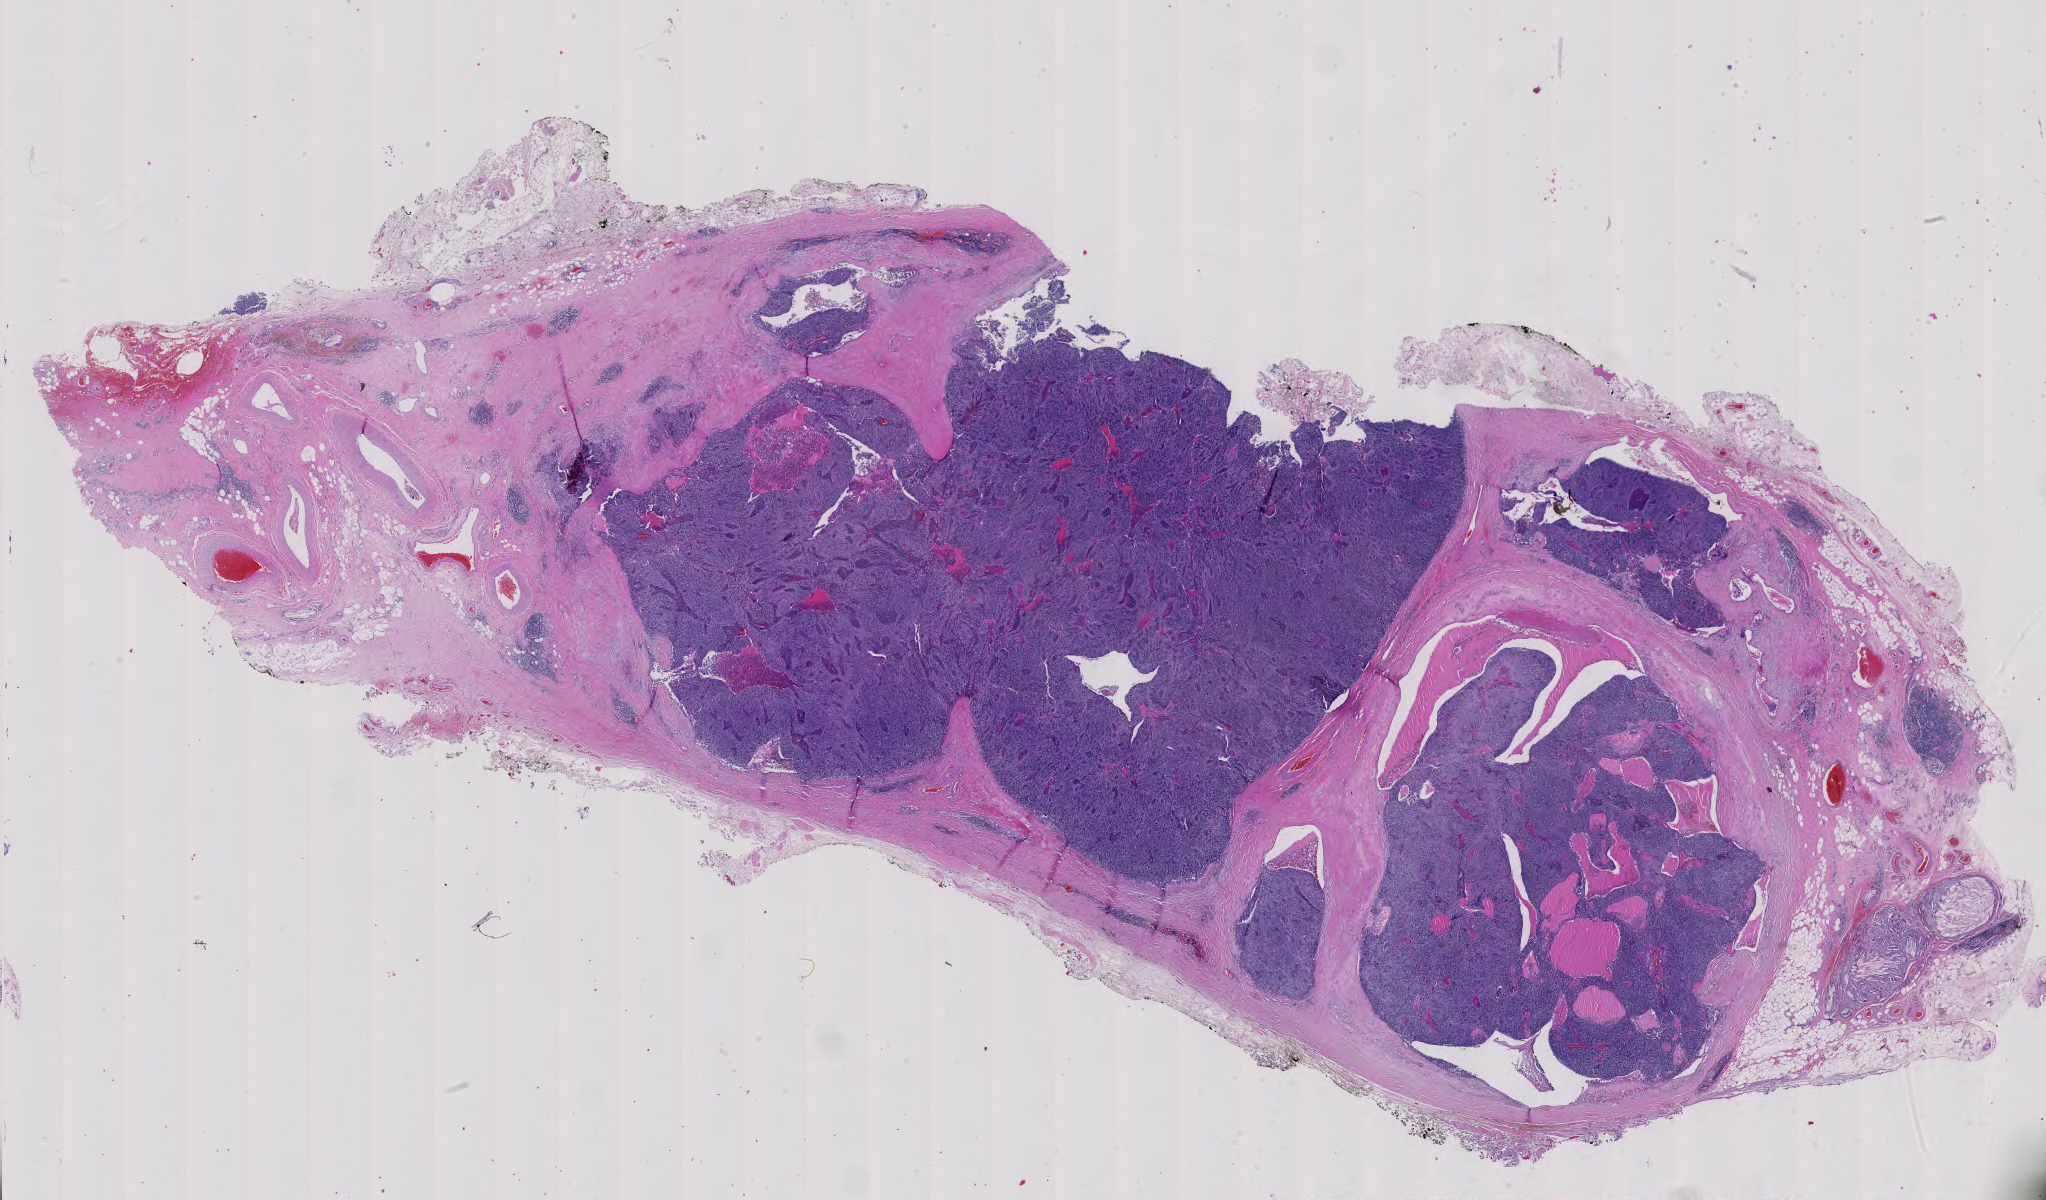
Digitized H&E tissue section (whole slide) — a low-resolution overview of the entire scanned area, about 29.8 x 17.5 mm. Formalin-fixed paraffin-embedded (FFPE) diagnostic section. Primary tumour sample from the thymus. Male, age 39 years at initial diagnosis.
* histologic diagnosis: Thymoma, type AB, malignant (anterior mediastinum)